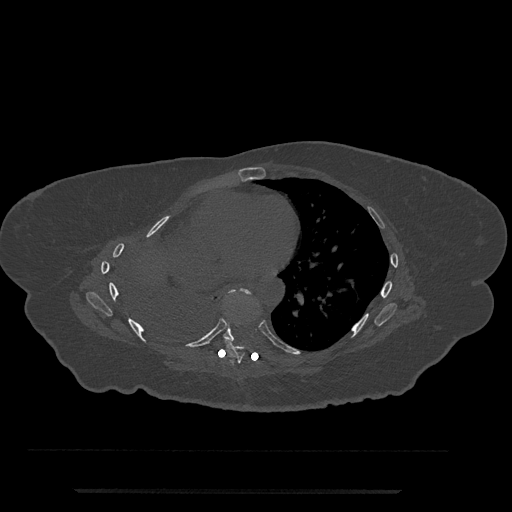
CT including the spine, one axial slice; position 421 of 797 along the scan axis; 120 kVp; bone window (W 1800 / L 400 HU); 0.5 mm slice thickness; 512 × 512 image matrix, field of view 440 × 440 mm. Female patient, age 51 years. From the clinical record (not read from this slice): primary cancer: neuro; vertebrae with lytic lesions (as recorded): T8.
Structures marked on this image (semi-automatically segmented with operator editing):
- T7 vertebra: bounding box (x1, y1, x2, y2) in pixels: (223, 339, 245, 363)
- T8 vertebra: (223, 289, 251, 342)